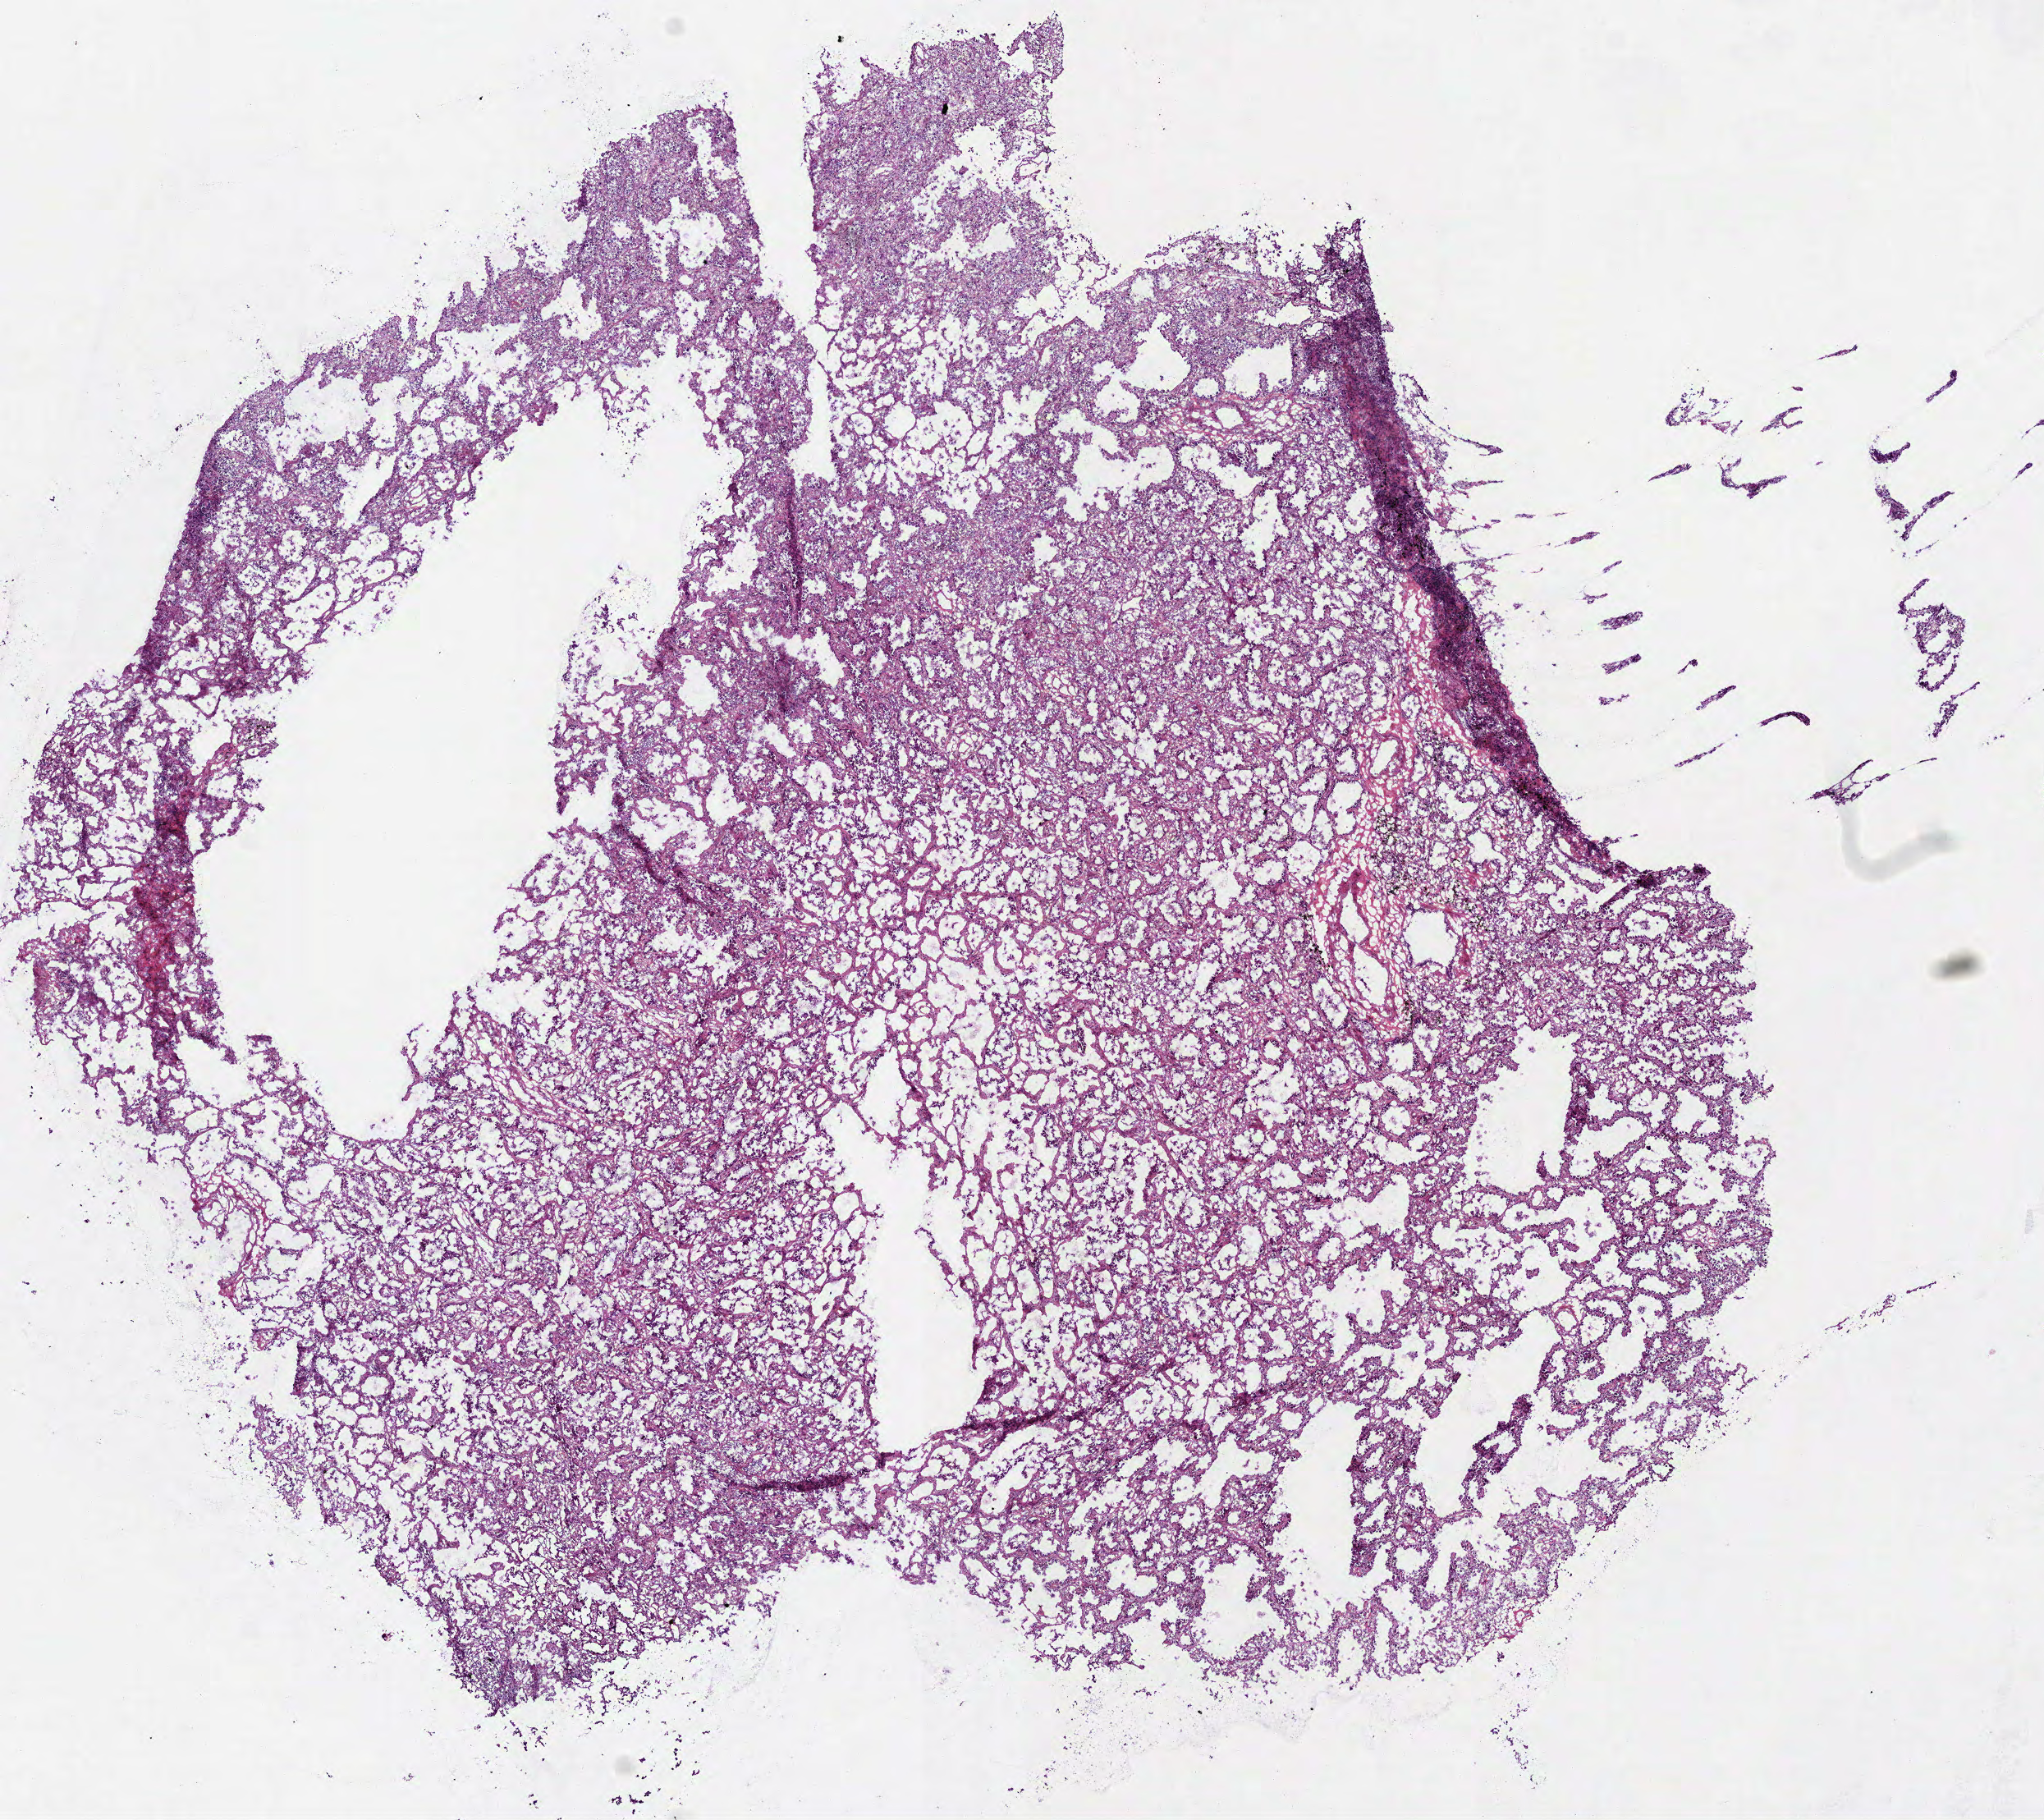
Hematoxylin and eosin (H&E) stained whole-slide image, whole scanned area (about 10.0 x 8.9 mm, slide scanned at 40x) shown as a low-resolution overview, frozen section from the top of the tissue portion, lung, primary tumour sample. Female, age 69 years at initial diagnosis. Composition of this section per pathologist review: tumour cells 100%, tumour nuclei 80%, normal cells 0%, stromal cells 0%, necrosis 0%. Inflammatory infiltration, as recorded: lymphocyte infiltration 7%, monocyte infiltration 7%, neutrophil infiltration 0%.
Laterality: right. Pathologic diagnosis: Acinar cell carcinoma (upper lobe, lung). AJCC pathologic stage: IA (7th edition).